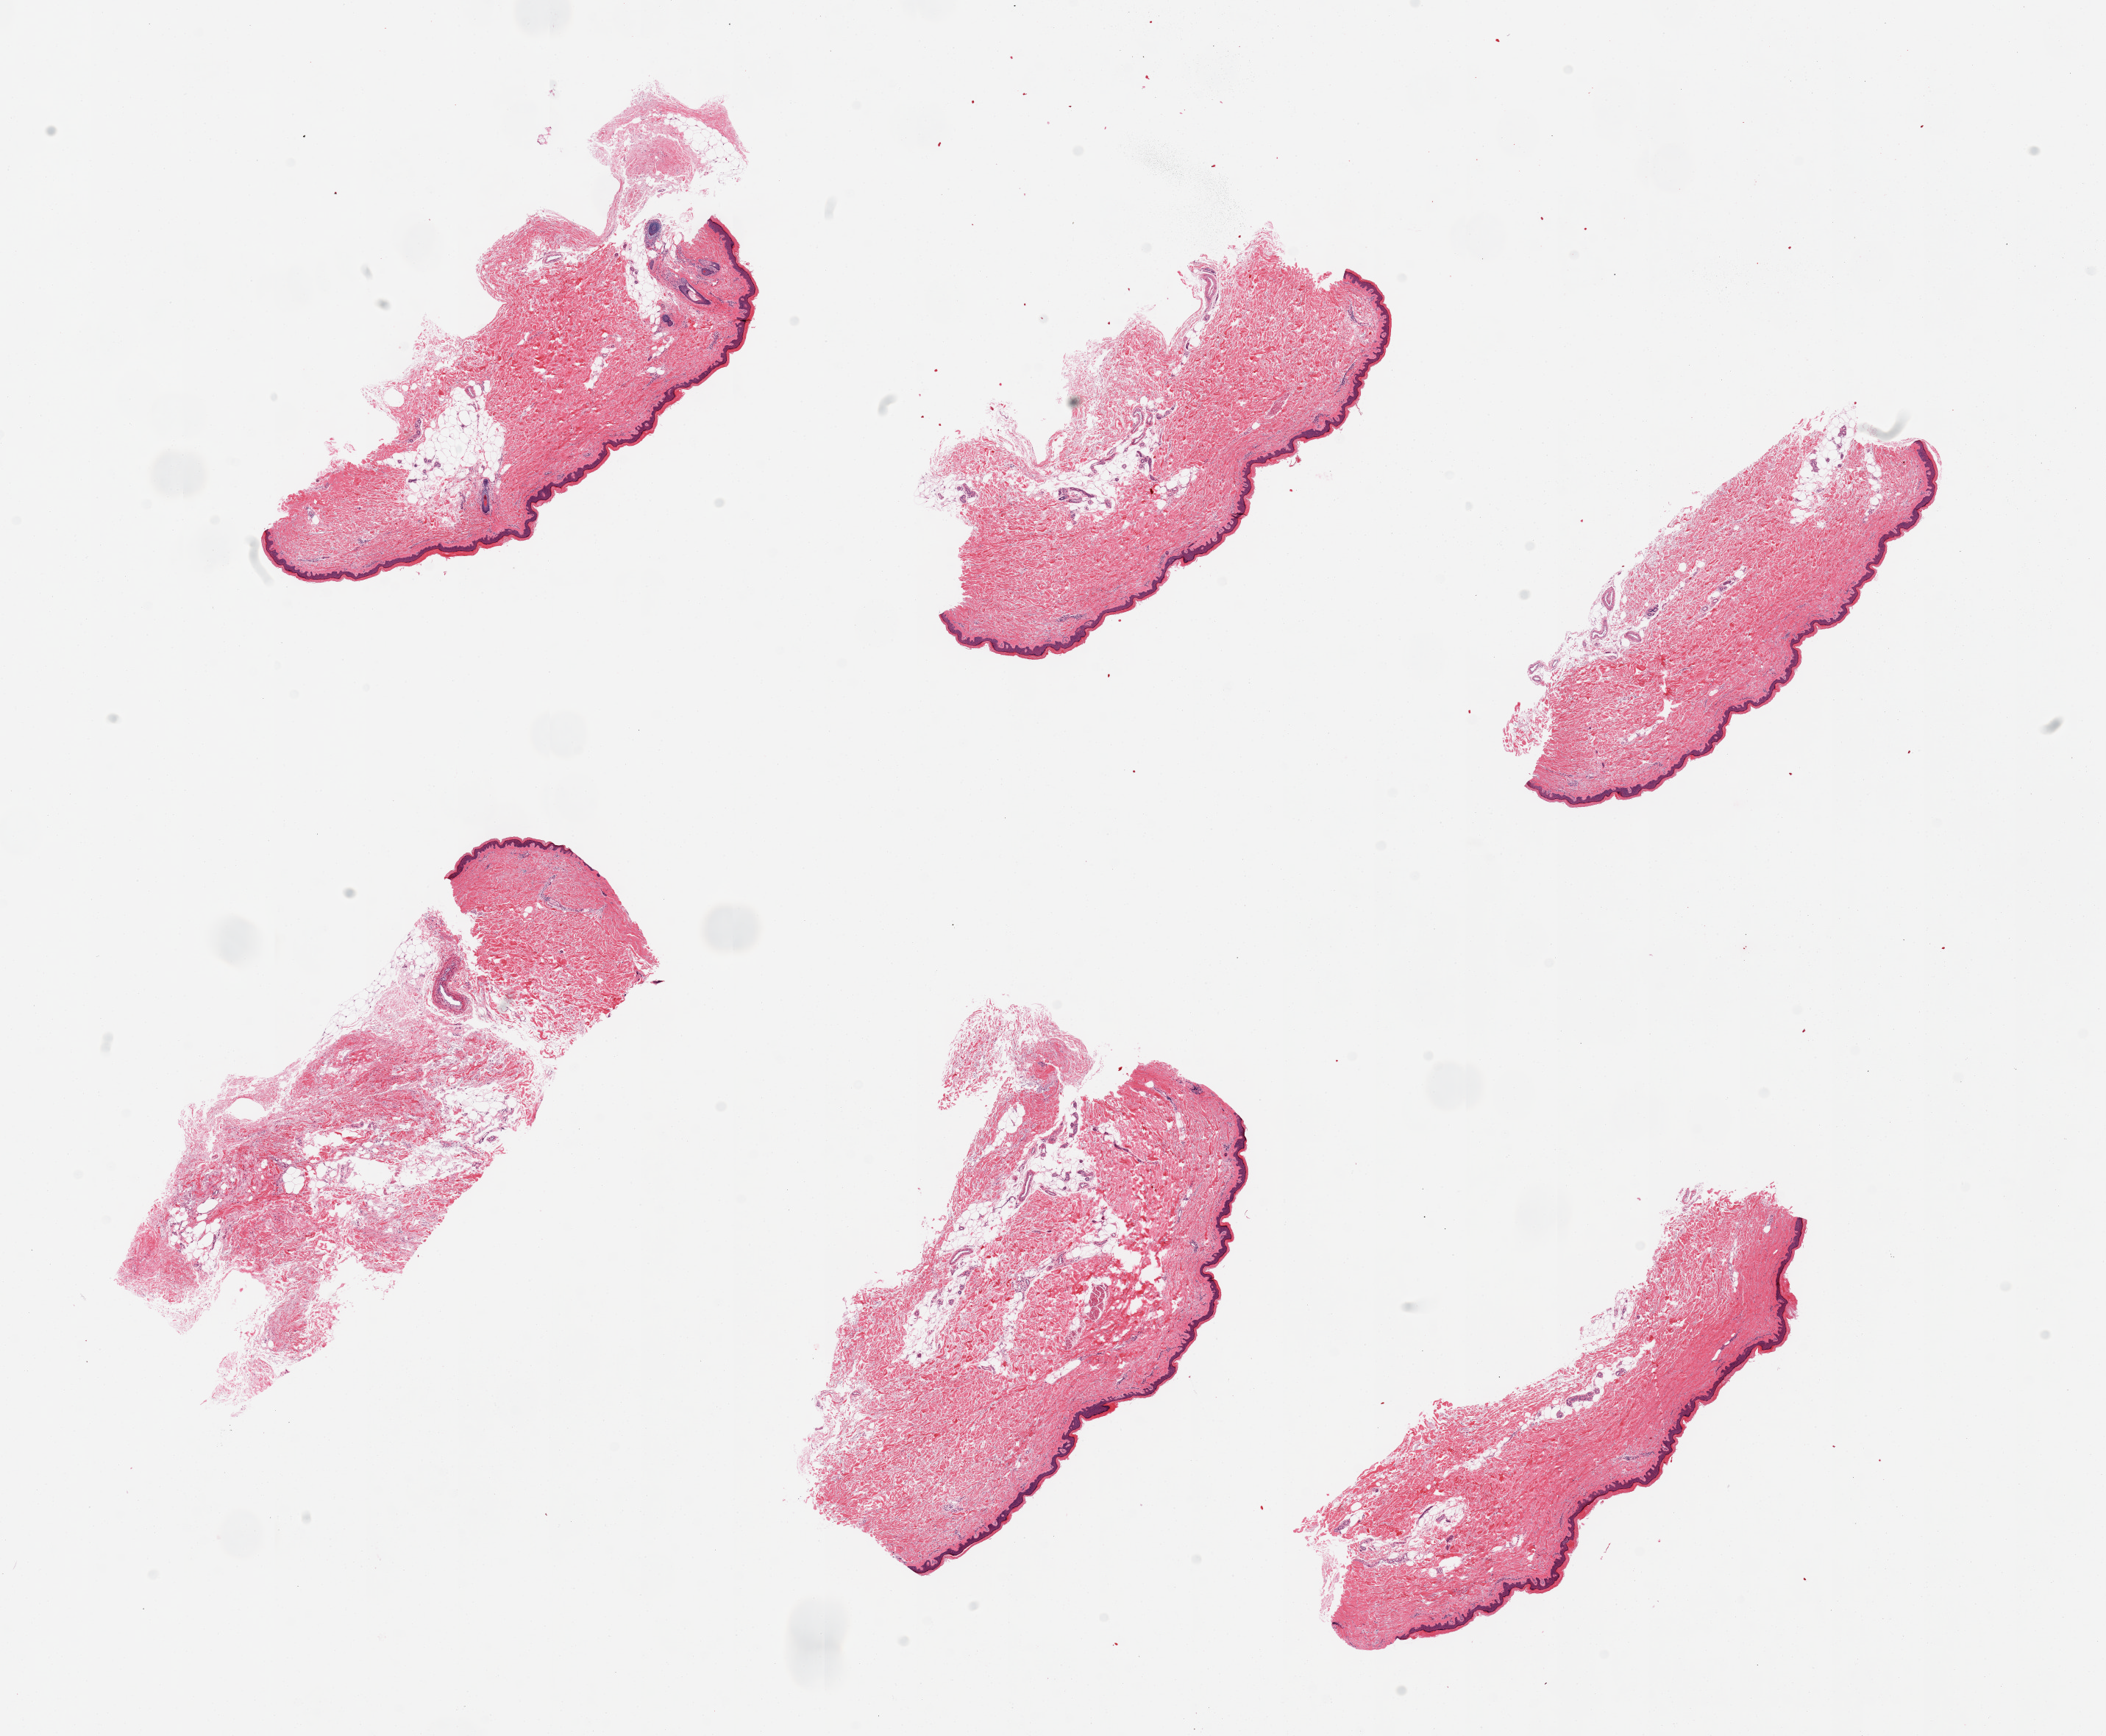
Digitized hematoxylin and eosin (H&E)-stained section, whole scanned area (about 22.6 x 18.7 mm) shown as a low-resolution overview. PAXgene-fixed paraffin-embedded (PFPE) section. Target tissue: skin of lower leg. Donor tissue sample. Female donor.
Review note (as recorded): 6 pieces, 5-10% predominantly internal fat, squamous epithelium measures ~45 microns.